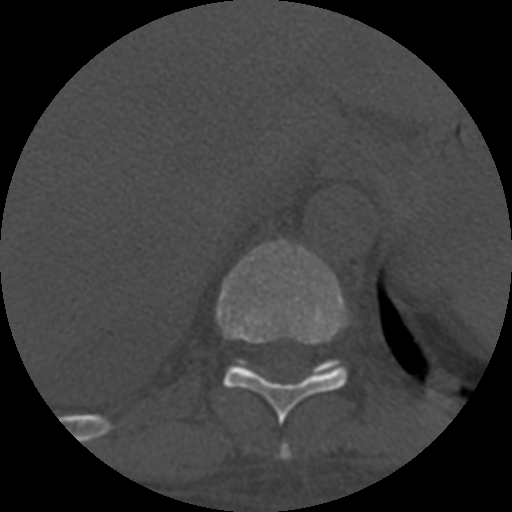
CT including the spine, one axial slice; reconstruction kernel STANDARD; one of 3 acquisitions stored at this slice position; bone window (W 1800 / L 400 HU); 1.25 mm slice thickness; 512 × 512 image matrix. Patient age 55 years. Case-level facts recorded for this patient, not image findings: primary cancer: colon; vertebrae with lytic lesions (as recorded): T12, L1, L5.
Annotated regions visible in this slice (semi-automatically segmented with operator editing):
- T10 vertebra: bounding box [x1, y1, x2, y2] px = [216, 239, 348, 424]
- T11 vertebra: [233, 360, 345, 377]
- T9 vertebra: [279, 443, 291, 460]